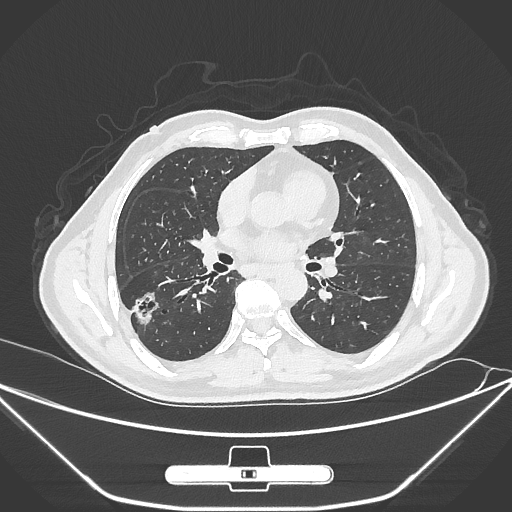
Chest CT, one axial slice. Position 148 of 310 along the scan axis. Reconstruction kernel IMR1,SharpPlus. 120 kVp. Lung window (W 1500 / L -600 HU). 1 mm slice thickness. 512 × 512 image matrix, field of view 398 × 398 mm. Patient: male, 71 years. Case-level facts recorded for this patient, not image findings: clinical TNM (as recorded): T1c N0 M0.
Outlined on this slice (bounding box drawn by a radiologist):
- lung tumour (recorded histology: adenocarcinoma): bounding box (x1, y1, x2, y2) in pixels: (125, 286, 160, 329)